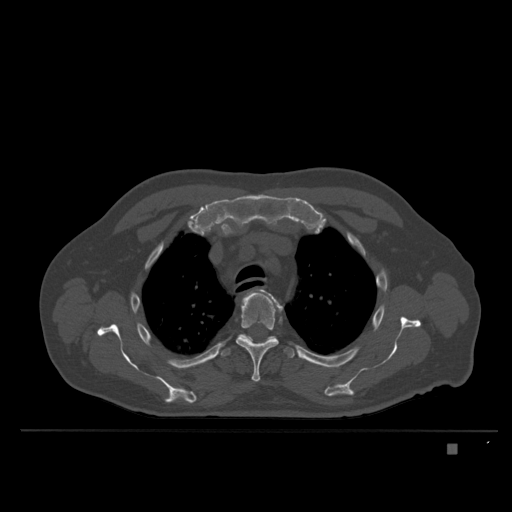
CT including the spine, one axial slice. Slice 286 of 435 in the series (ordered by position). Bone window (W 1800 / L 400 HU). 1.5 mm slice thickness. 512 × 512 image matrix, field of view 434 × 434 mm. Patient: male, 73 years. Case-level facts recorded for this patient, not image findings: primary cancer: skin.
Outlined on this slice (semi-automatic segmentation, software-assisted and operator-edited):
- T3 vertebra: bounding box (x1, y1, x2, y2) in pixels: (248, 290, 282, 308)
- T4 vertebra: (236, 292, 278, 382)
- T5 vertebra: (221, 334, 294, 358)